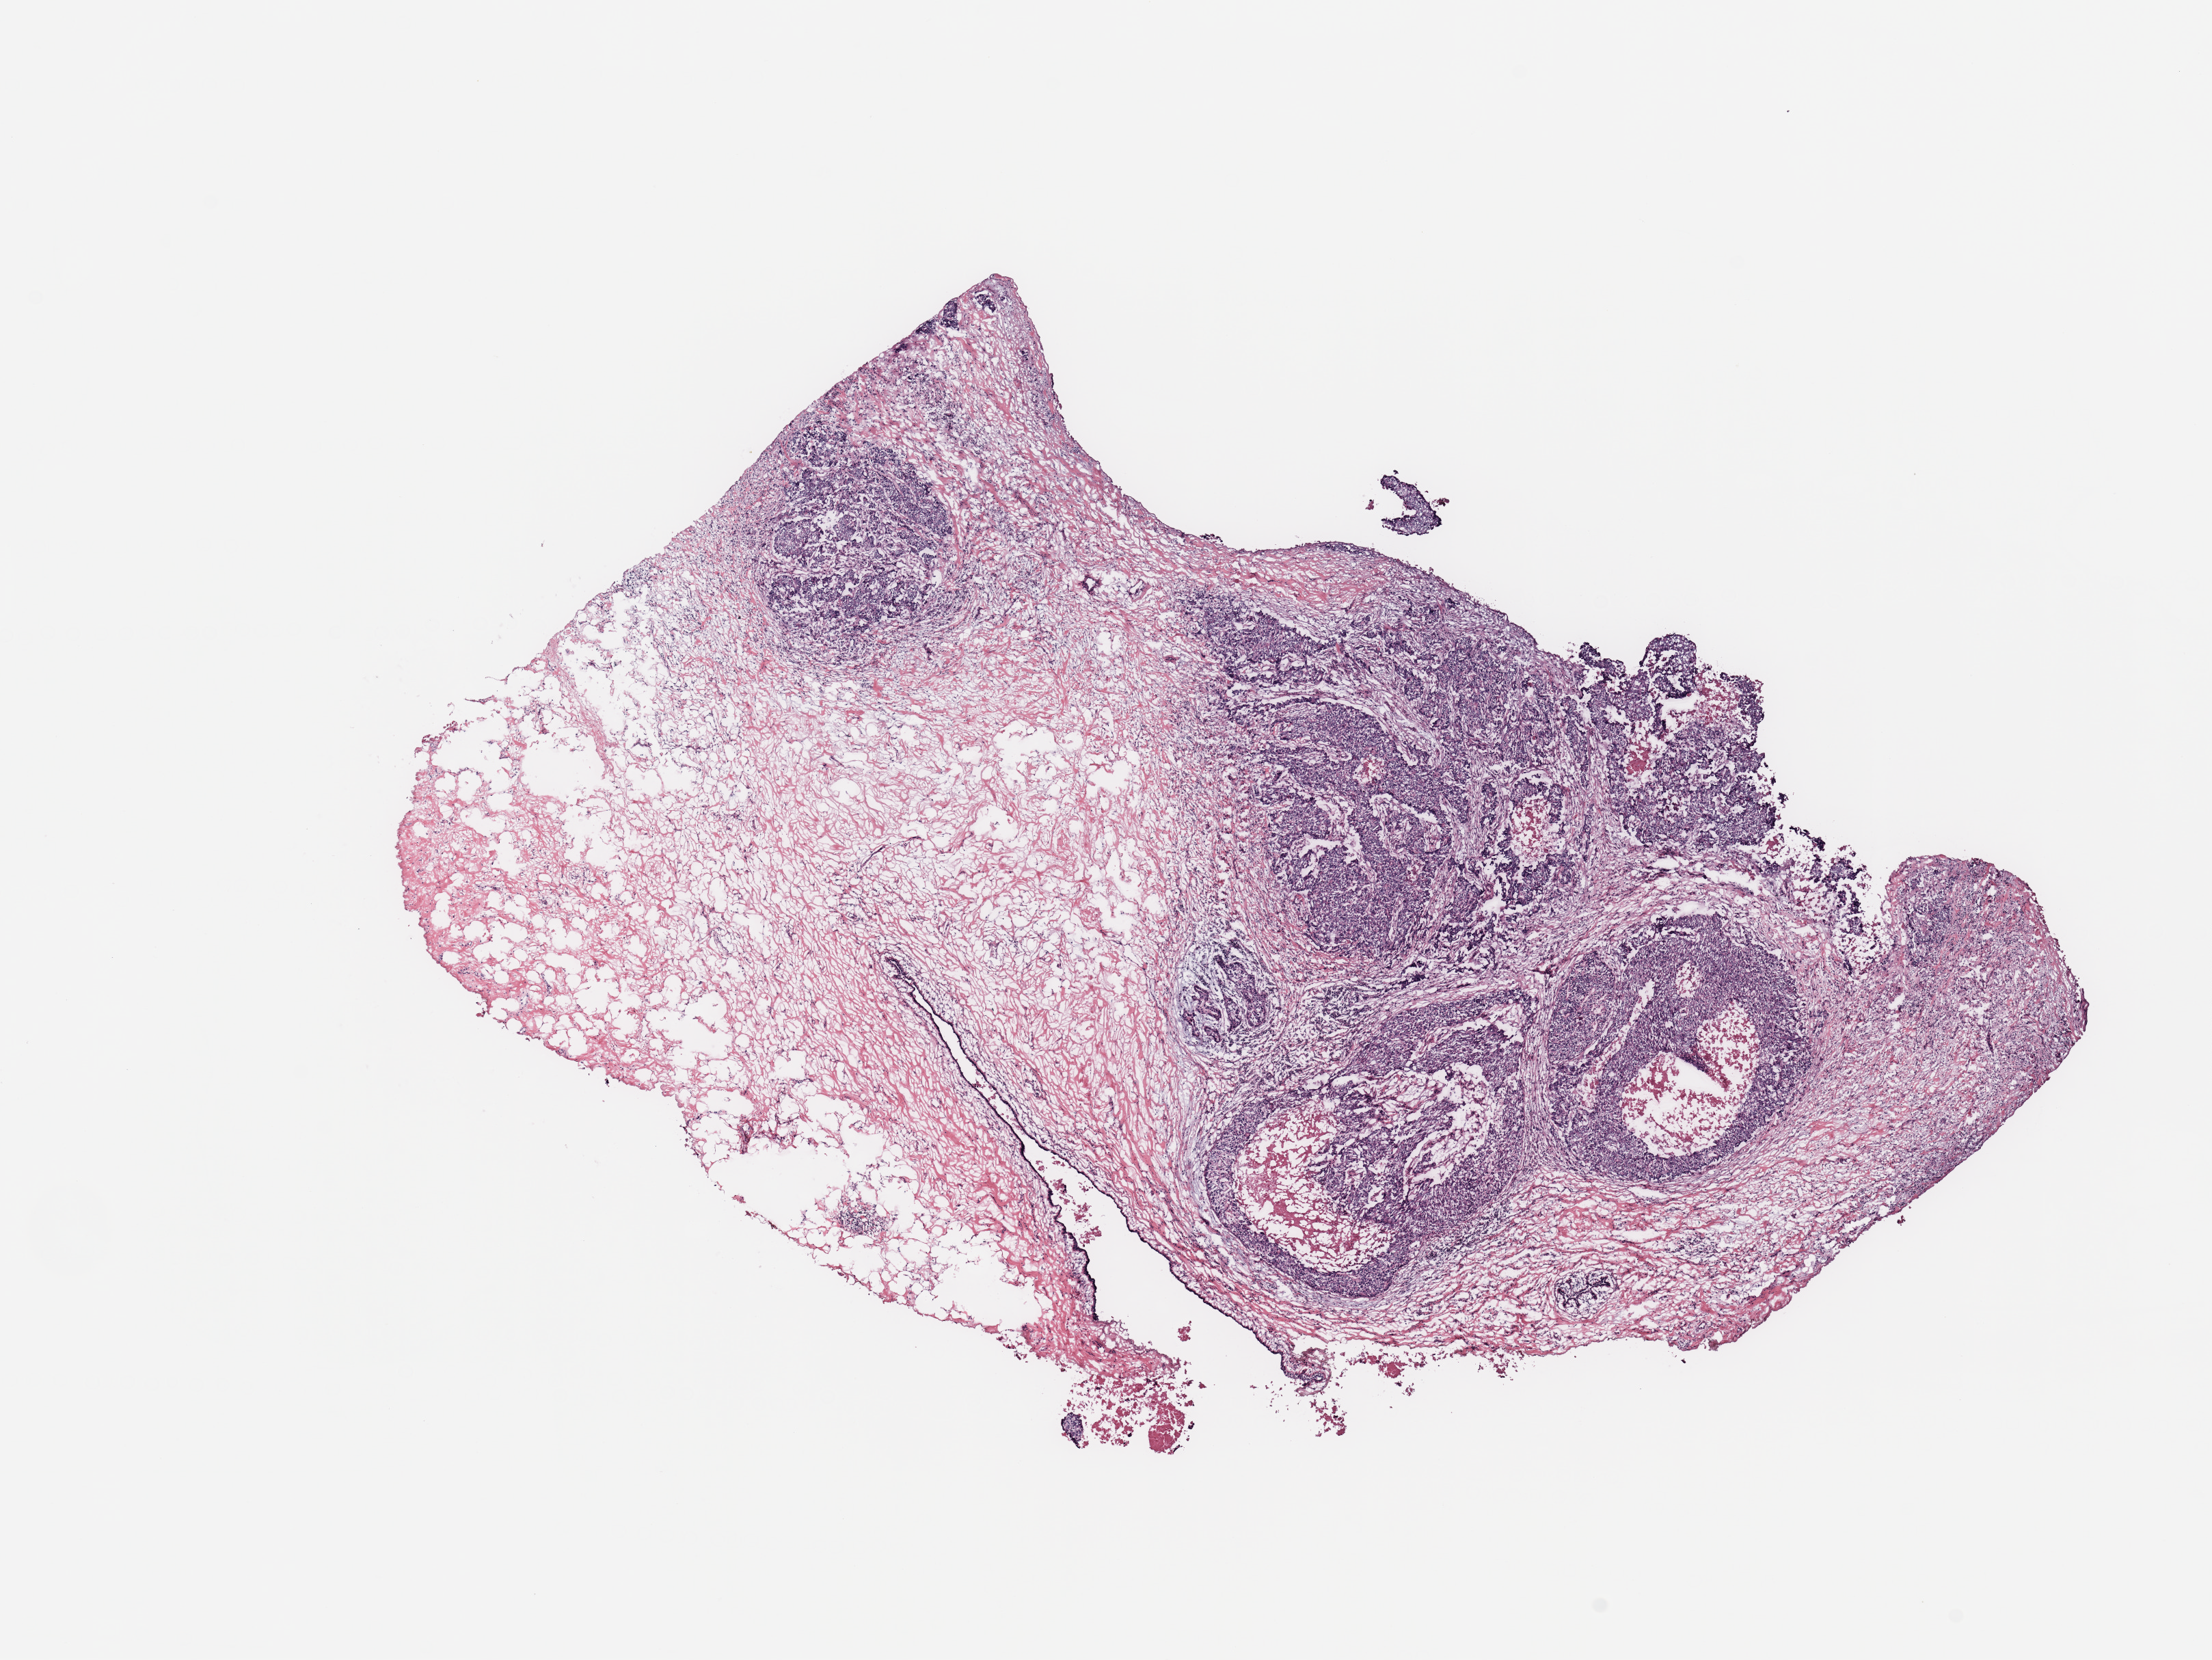
Digitized H&E tissue section (whole slide), low-resolution overview of the scanned area, about 12.8 x 9.6 mm (acquisition: 20x scan). Breast, tissue type not recorded.
Patient diagnosis (cohort enrolment): breast cancer (breast).